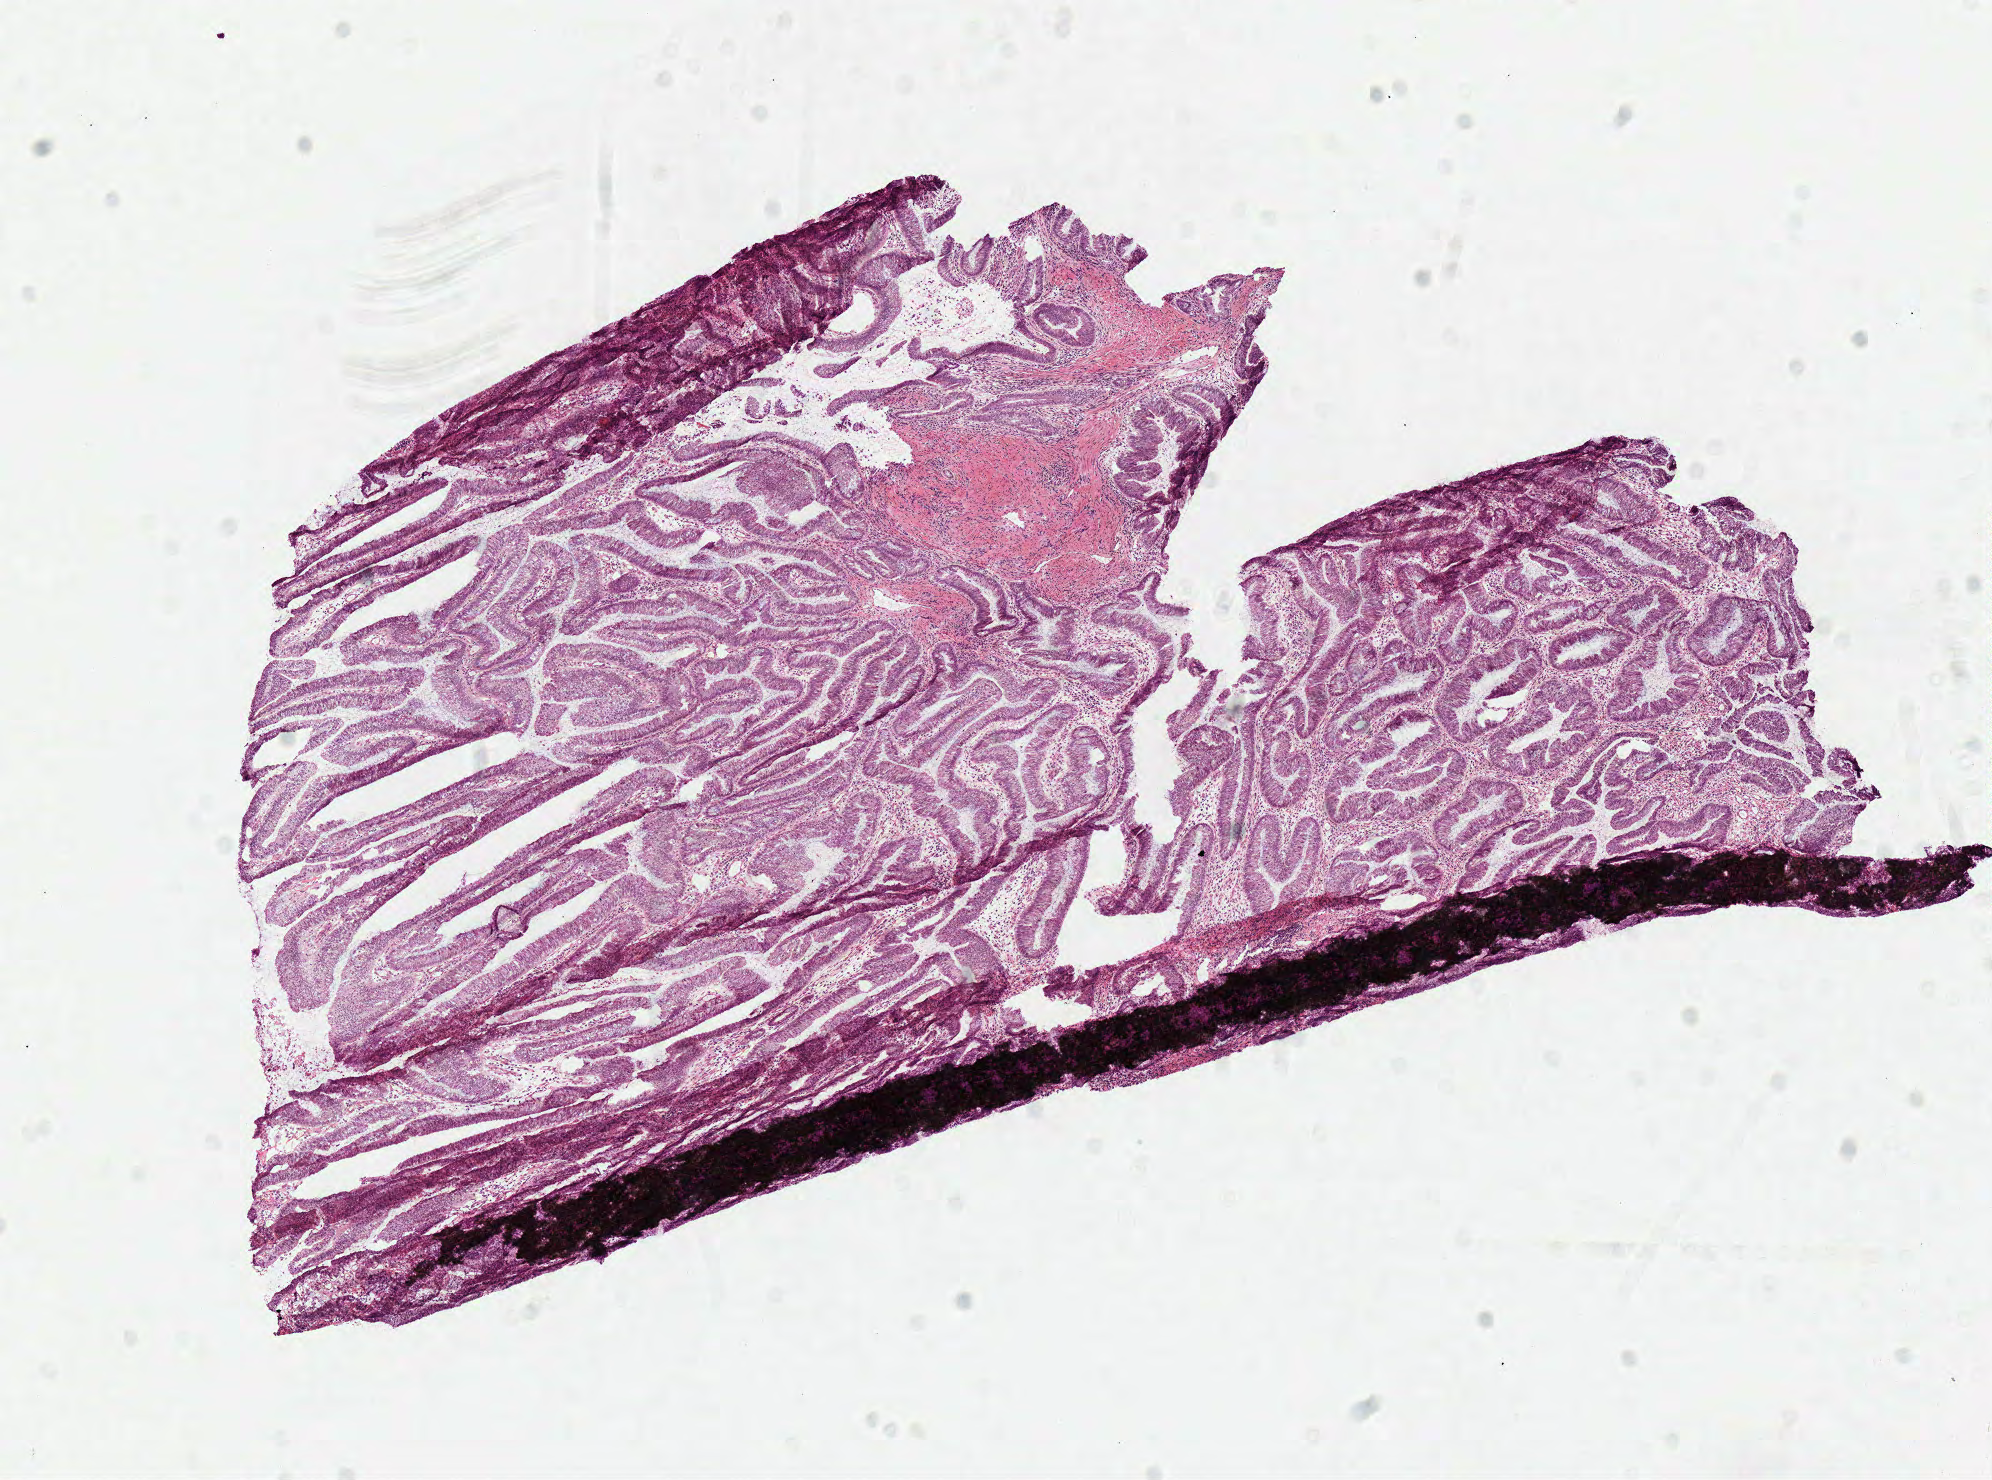
Whole-slide histology image, Hematoxylin and eosin (H&E) stained — whole scanned area (about 7.8 x 5.8 mm, from a 40x scan) shown as a low-resolution overview. Frozen section from the top of the tissue portion. Primary tumour sample from the colon. Male patient; age at initial diagnosis 65 years. Slide review estimates, as recorded: tumour cells 88%, tumour nuclei 80%, normal cells 0%, stromal cells 12%, necrosis 0%.
• pathologic diagnosis: Mucinous adenocarcinoma
• lymph nodes positive (case pathology): 2 of 26 examined
• AJCC pathologic stage: IIIB
• TNM: T3 N1 MX